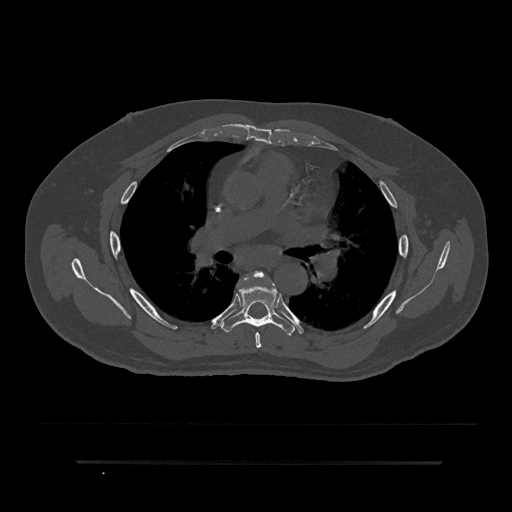
CT including the spine, one axial slice. Position 541 of 797 along the scan axis. Reconstruction kernel Br40s/3. 120 kVp. Bone window (W 1800 / L 400 HU). 512 × 512 image matrix. Male patient, age 59 years. From the clinical record (not read from this slice): primary cancer: bile ducts.
Annotated regions visible in this slice (semi-automatic segmentation, software-assisted and operator-edited):
- T5 vertebra: bounding box [x1, y1, x2, y2] px = [251, 271, 264, 348]
- T6 vertebra: [221, 284, 294, 335]